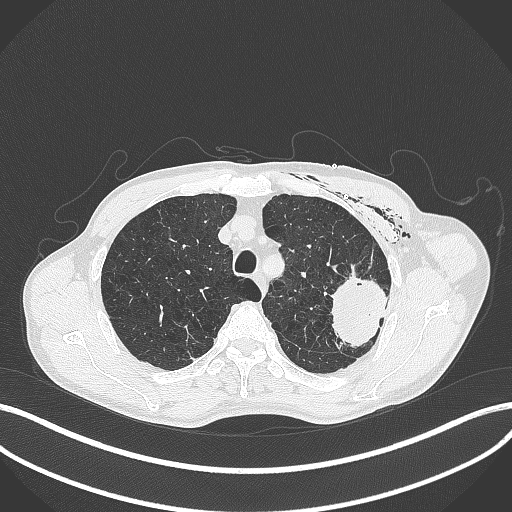
Chest CT, one axial slice; position 320 of 457 along the scan axis; reconstruction kernel B70f; 120 kVp; lung window (W 1500 / L -600 HU); 1 mm slice thickness; 512 × 512 image matrix, field of view 400 × 400 mm. Patient: male, 58 years. From the clinical record (not read from this slice): clinical TNM (as recorded): T3 N0 M0.
Annotated regions visible in this slice (rectangle marked by the reading radiologist):
- lung tumour (recorded histology: adenocarcinoma): bounding box <326,270,389,356> (left, top, right, bottom; pixels)